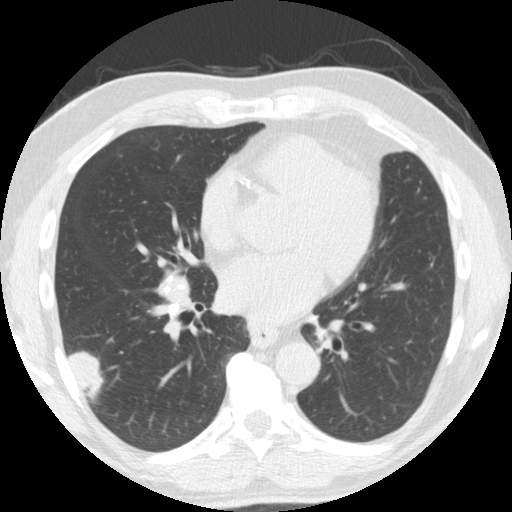
Low-dose screening chest CT, one axial slice; position 79 of 174 along the scan axis; reconstruction kernel STANDARD; lung window (W 1500 / L -600 HU); 2.5 mm slice thickness; 512 × 512 image matrix.
Outlined on this slice (manually delineated by an expert):
- lesion 1 (tumor, lower lobe of right lung): bounding box (x1, y1, x2, y2) in pixels: (68, 351, 105, 398)